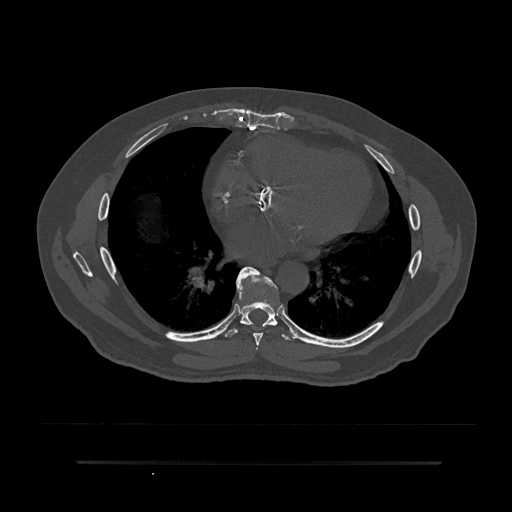
CT including the spine, one axial slice. Slice 452 of 797 in the series (ordered by position). Reconstruction kernel Br40s/3. 120 kVp. Bone window (W 1800 / L 400 HU). 0.5 mm slice thickness. 512 × 512 image matrix, field of view 464 × 464 mm. Male patient, age 59 years. Case-level facts recorded for this patient, not image findings: primary cancer: bile ducts; vertebrae with lytic lesions (as recorded): T10.
Structures marked on this image (semi-automatically segmented with operator editing):
- T7 vertebra: bounding box [x1, y1, x2, y2] px = [236, 266, 263, 346]
- T8 vertebra: [222, 270, 296, 340]